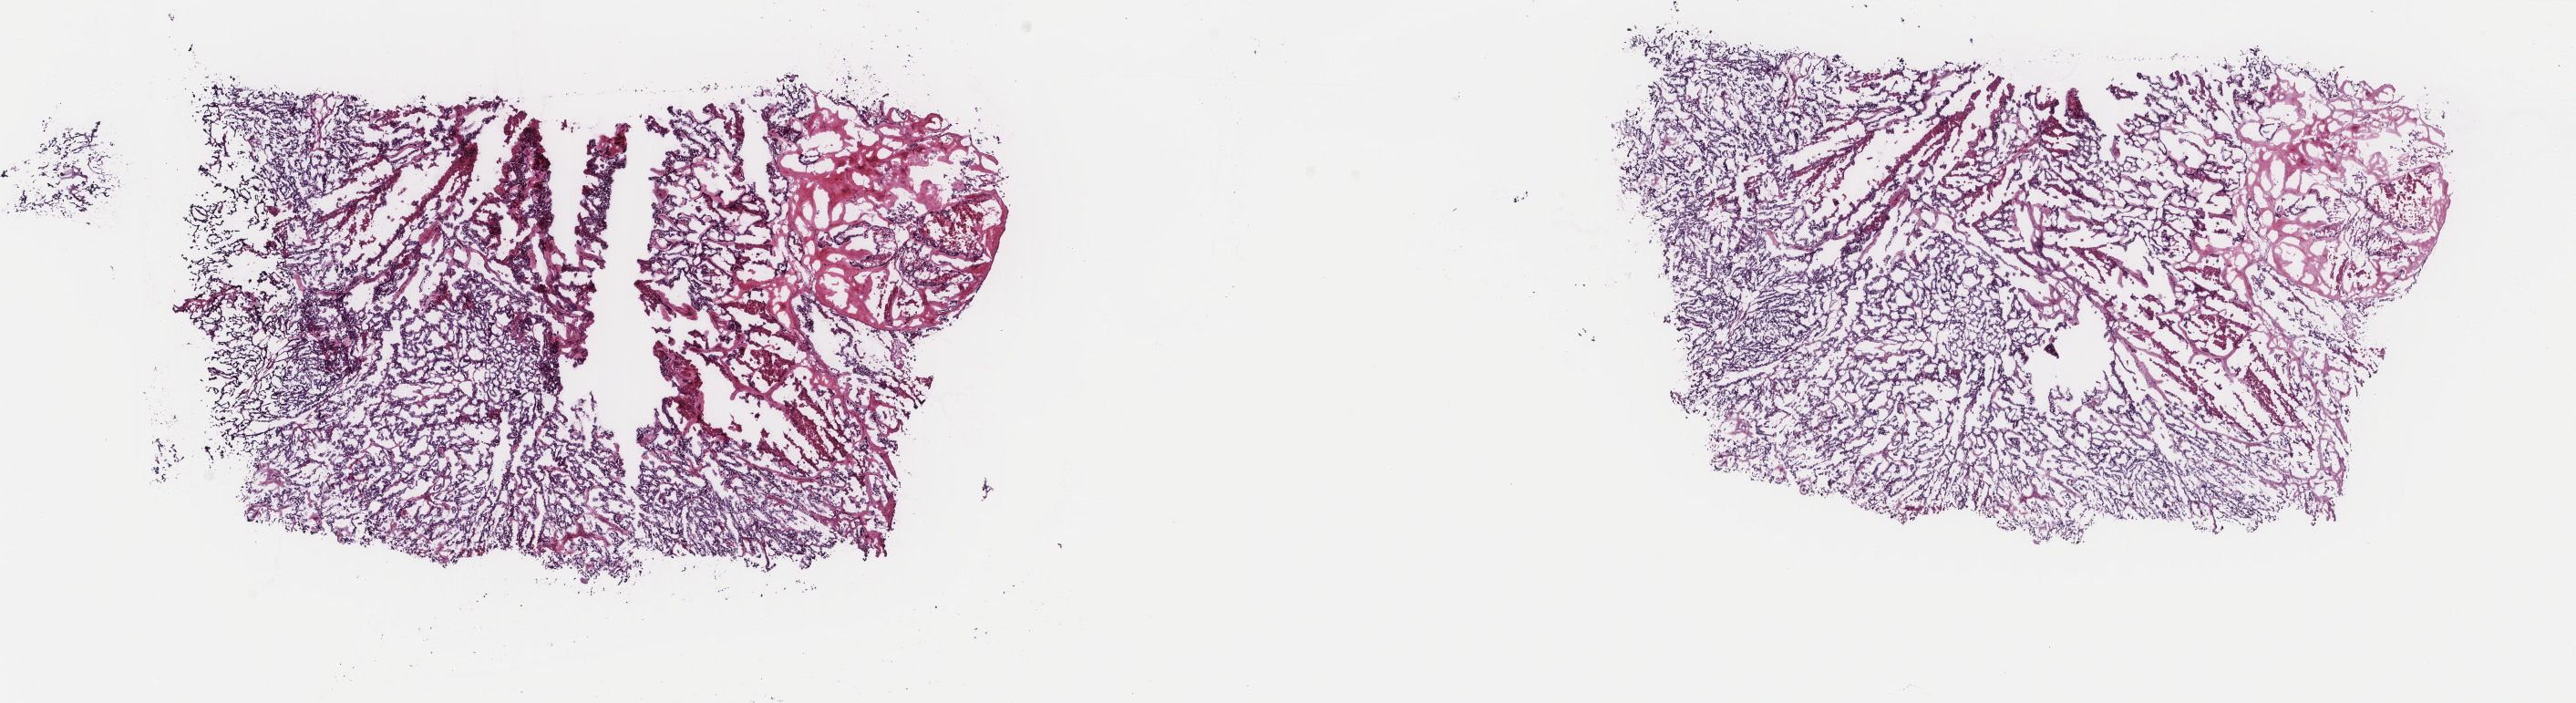
Digitized H&E tissue section (whole slide), a low-resolution overview of the entire scanned area, about 22.4 x 6.1 mm. Frozen section. Uterus, primary tumour sample. Female patient; age at initial diagnosis 63 years. Histologic grade: G3 (poorly differentiated). Composition of this section per pathologist review: tumour cells 85%, tumour nuclei 85%, normal cells 0%, stromal cells 5%, necrosis 10%. Infiltration values recorded for this section: lymphocyte infiltration 40%, monocyte infiltration 20%, neutrophil infiltration 20%.
• FIGO stage: IIIA
• diagnosis: Serous cystadenocarcinoma, NOS (endometrium)